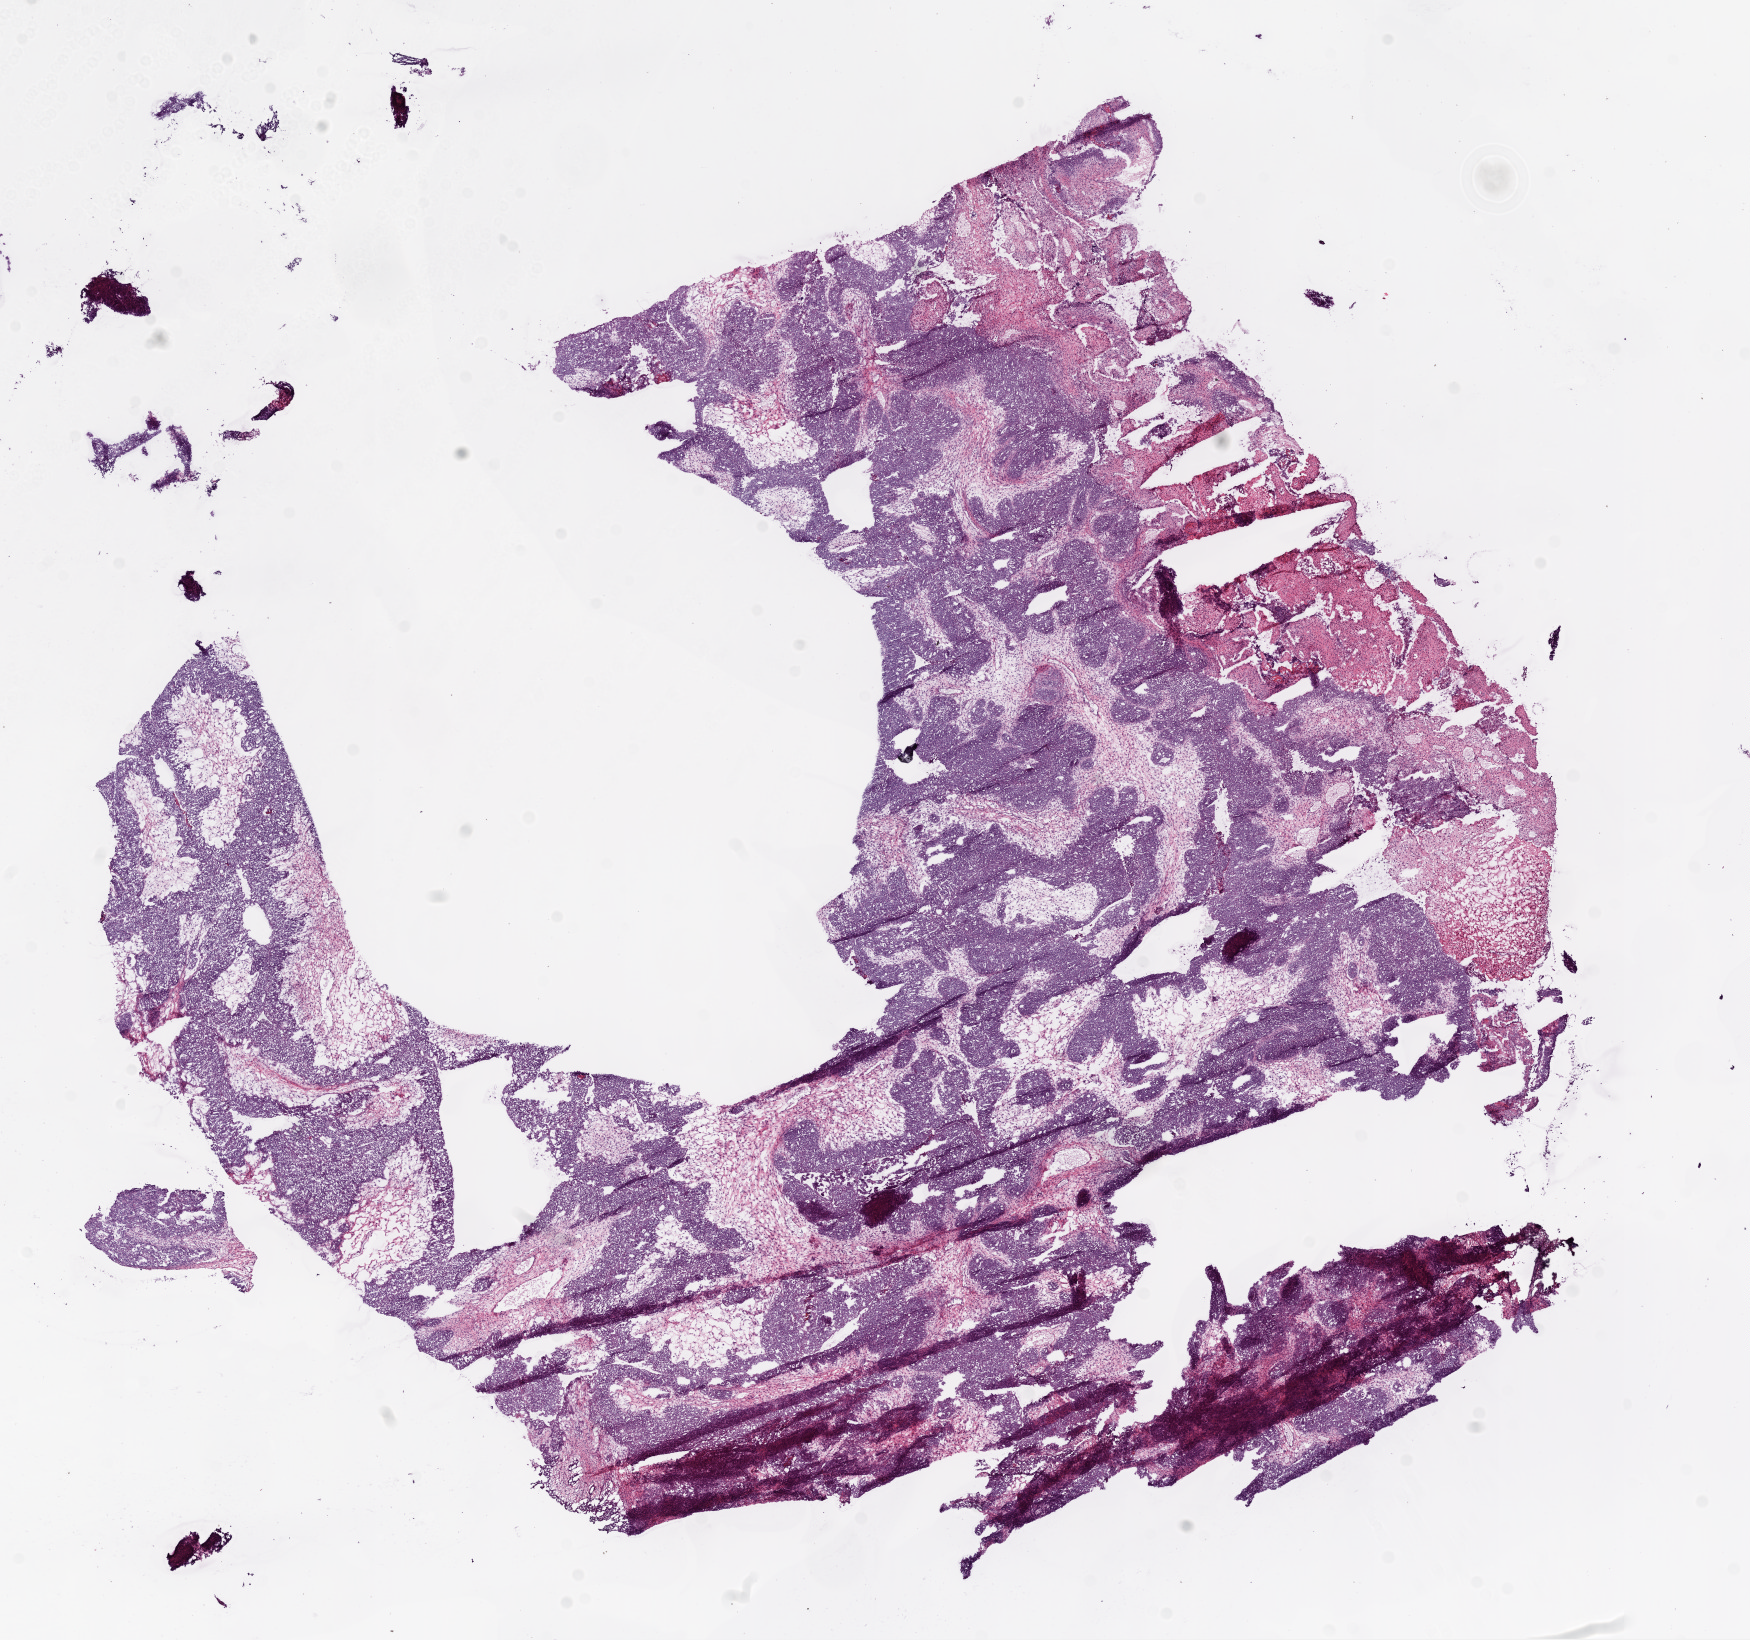
Digitized H&E tissue section (whole slide) — shown as a low-resolution overview of the whole scanned area (about 14.0 x 13.2 mm). Frozen section from the bottom of the tissue portion. Sample: primary tumour, ovary. Female patient; age at initial diagnosis 45 years. Histologic grade: G3 (poorly differentiated). Slide review estimates, as recorded: tumour cells 60%, tumour nuclei 95%, normal cells 0%, stromal cells 39%, necrosis 1%.
Diagnosis: Serous cystadenocarcinoma, NOS. FIGO stage: IIIC. Laterality: bilateral.